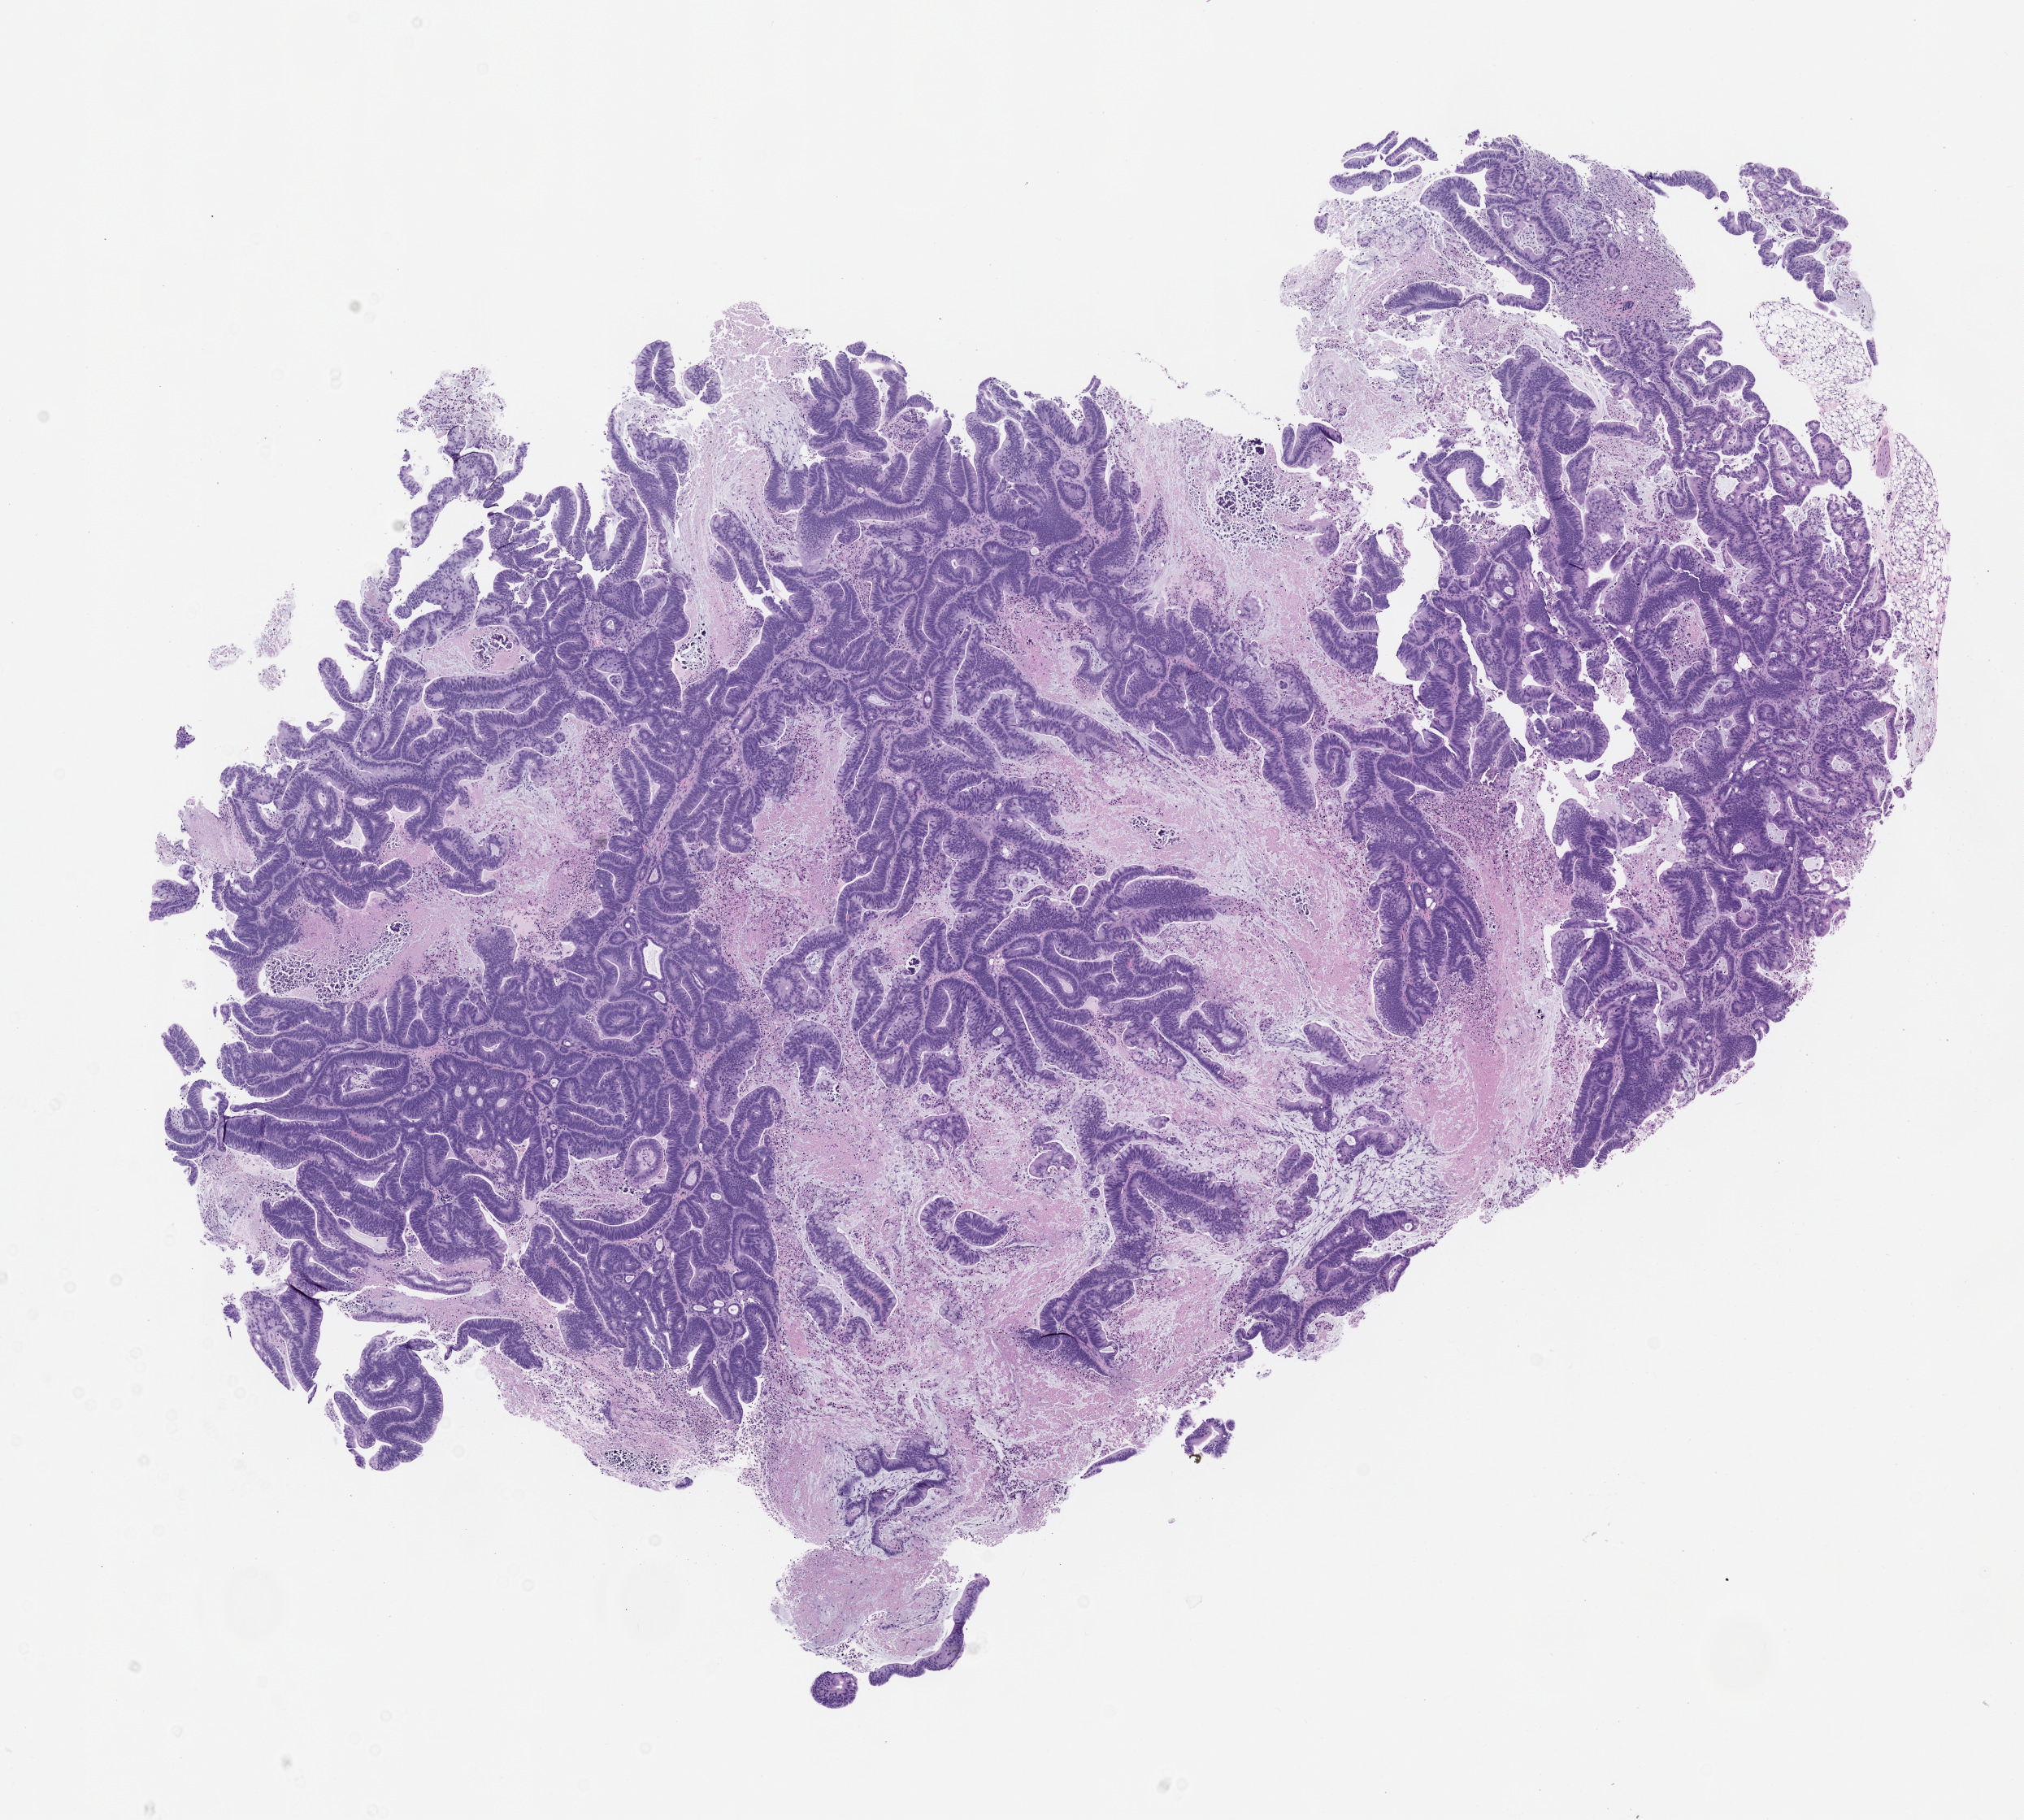
Whole-slide image, hematoxylin and eosin (H&E): patient-derived xenograft (human tumor grown in a mouse), passage 2 — shown as a low-resolution overview of the whole scanned area (about 10.0 x 9.0 mm); FFPE section; tumor site category: colon.
Originating patient diagnosis: Colon Adenocarcinoma.